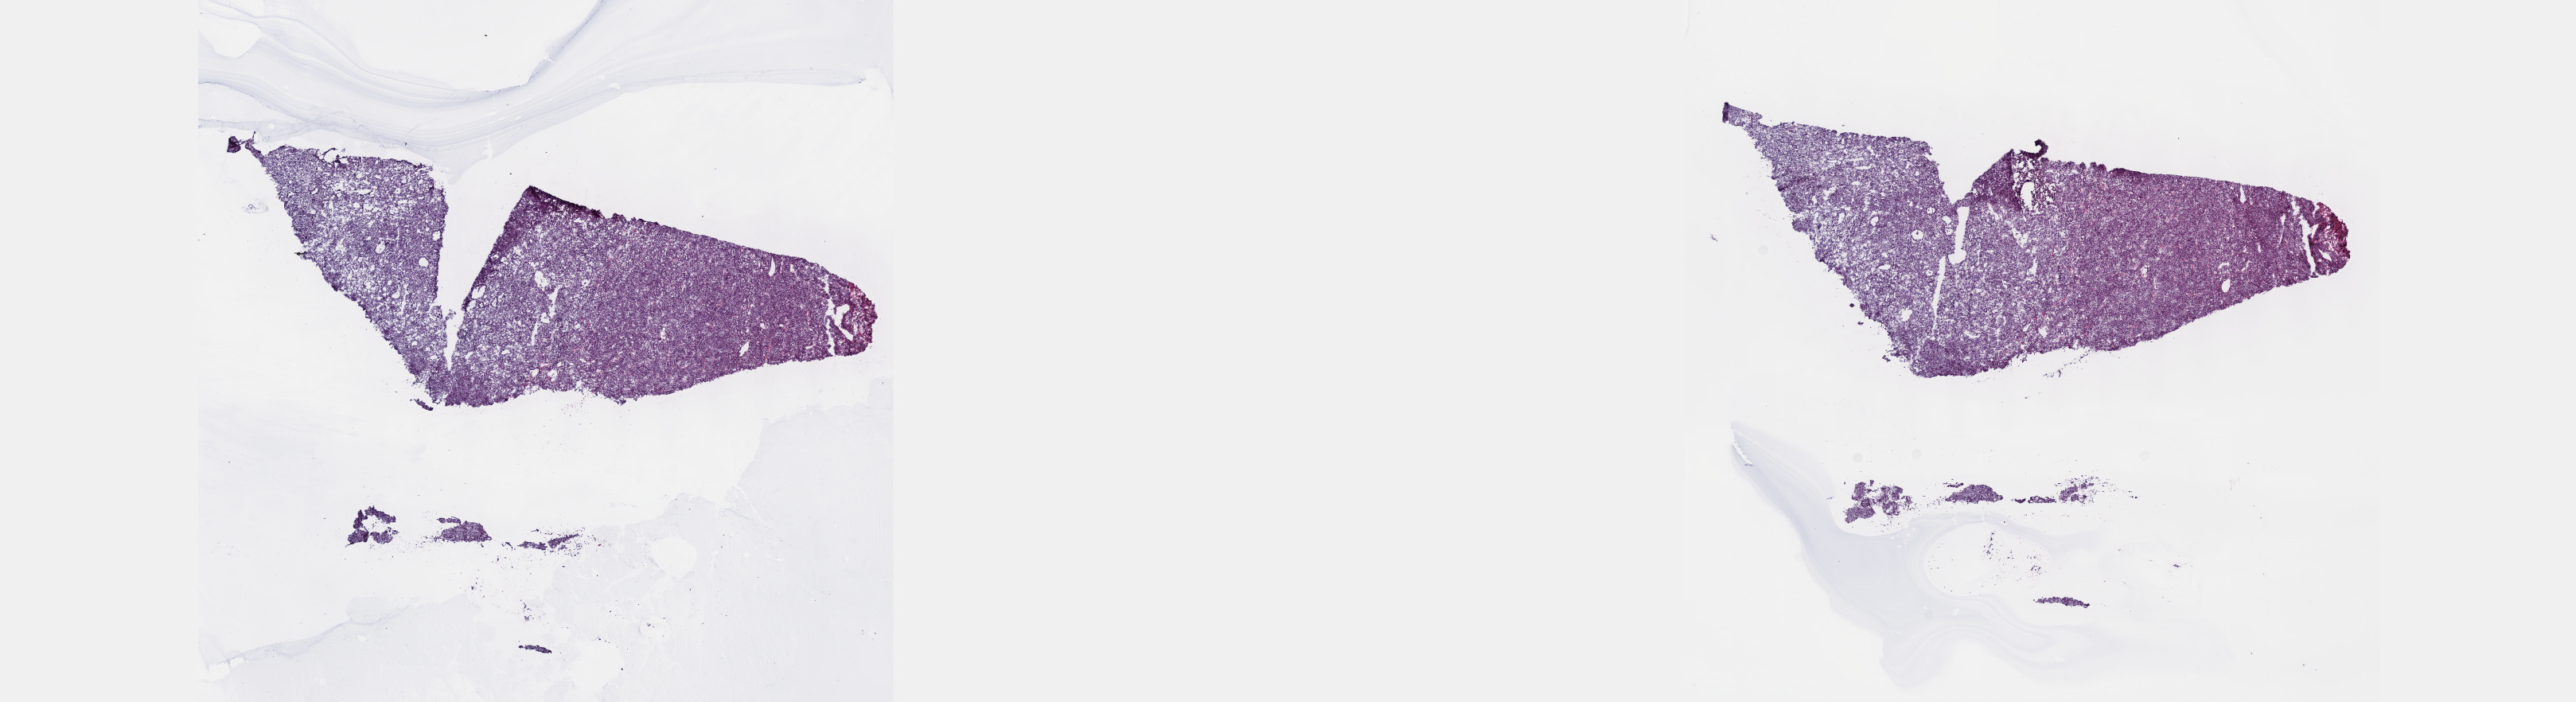
Digitized H&E-stained tissue section (whole slide), low-resolution overview of the scanned area, about 26.2 x 7.1 mm. Frozen section from the top of the tissue portion. Sample: primary tumour, kidney. Patient: female, age at initial diagnosis 47 years. Histologic grade: G1 (well differentiated). Pathologist review of this section (percent, as recorded): tumour cells 85%, tumour nuclei 85%, normal cells 0%, stromal cells 15%, necrosis 0%. Infiltration values recorded for this section: lymphocyte infiltration 3%, monocyte infiltration 0%, neutrophil infiltration 0%.
• AJCC pathologic stage: I (7th edition)
• pathologic diagnosis: Clear cell adenocarcinoma, NOS